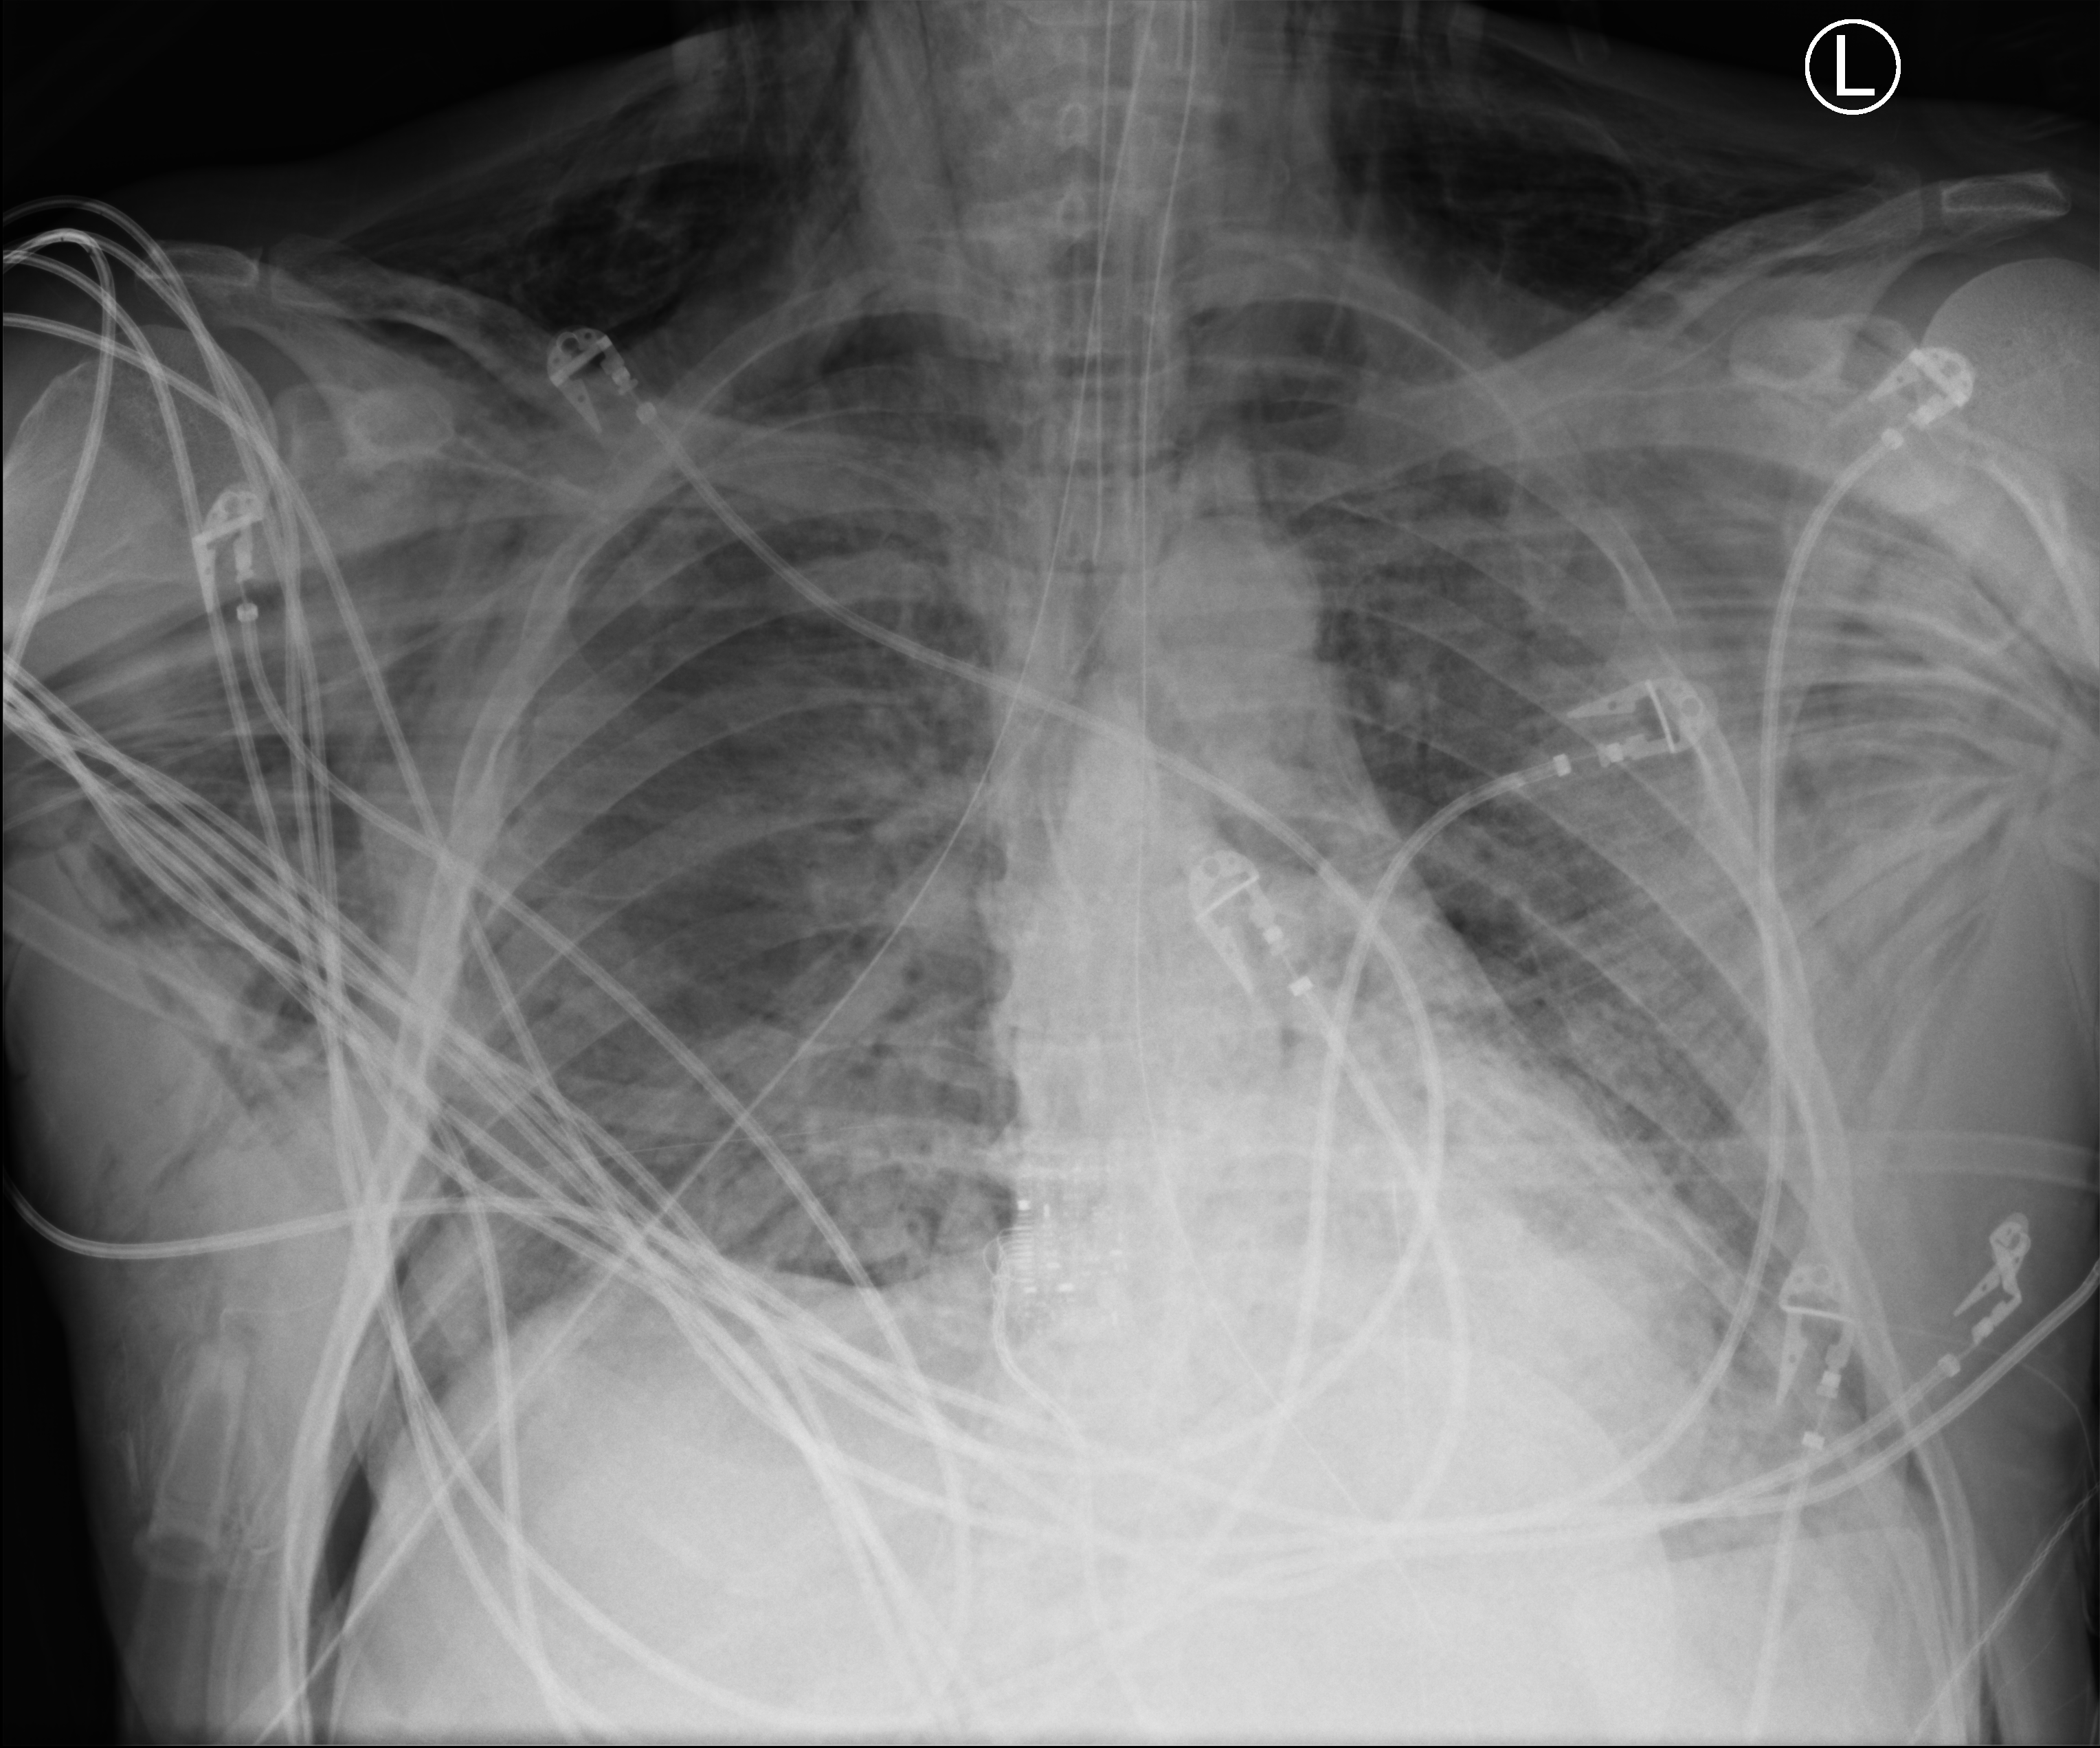
Chest X-ray (portable), anteroposterior (AP) projection. Male patient hospitalised with COVID-19, age 18–59 years.
Admission-level facts for this patient (not findings on this image; timing relative to this image not recorded):
- admitted to intensive care during this hospital stay: yes
- mechanically ventilated during this hospital stay: yes